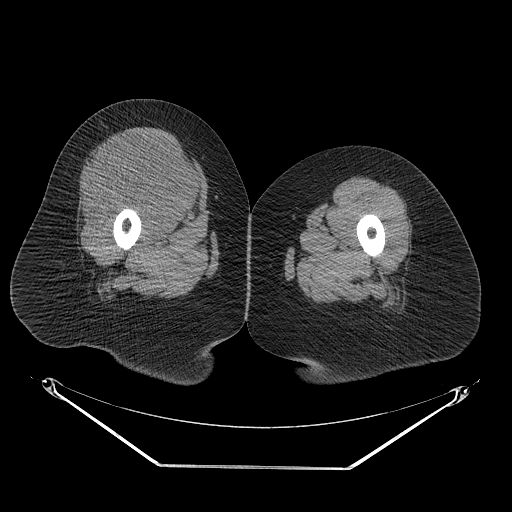
CT of an extremity soft-tissue mass (from a PET/CT study), one axial slice; position 34 of 267 along the scan axis; reconstruction kernel STANDARD; 140 kVp; soft-tissue window (W 400 / L 40 HU); 512 × 512 image matrix, field of view 500 × 500 mm. Female patient. From the clinical record (not read from this slice): histological type: malignant solitary fibrous tumor; grade: intermediate; site of the primary tumour: right thigh.
Outlined on this slice (expert contour drawn on MRI and transferred to this co-registered scan by the dataset authors):
- gross tumour volume including surrounding oedema: bounding box [x1, y1, x2, y2] px = [87, 132, 207, 225]
- gross tumour volume (mass): [94, 132, 204, 220]